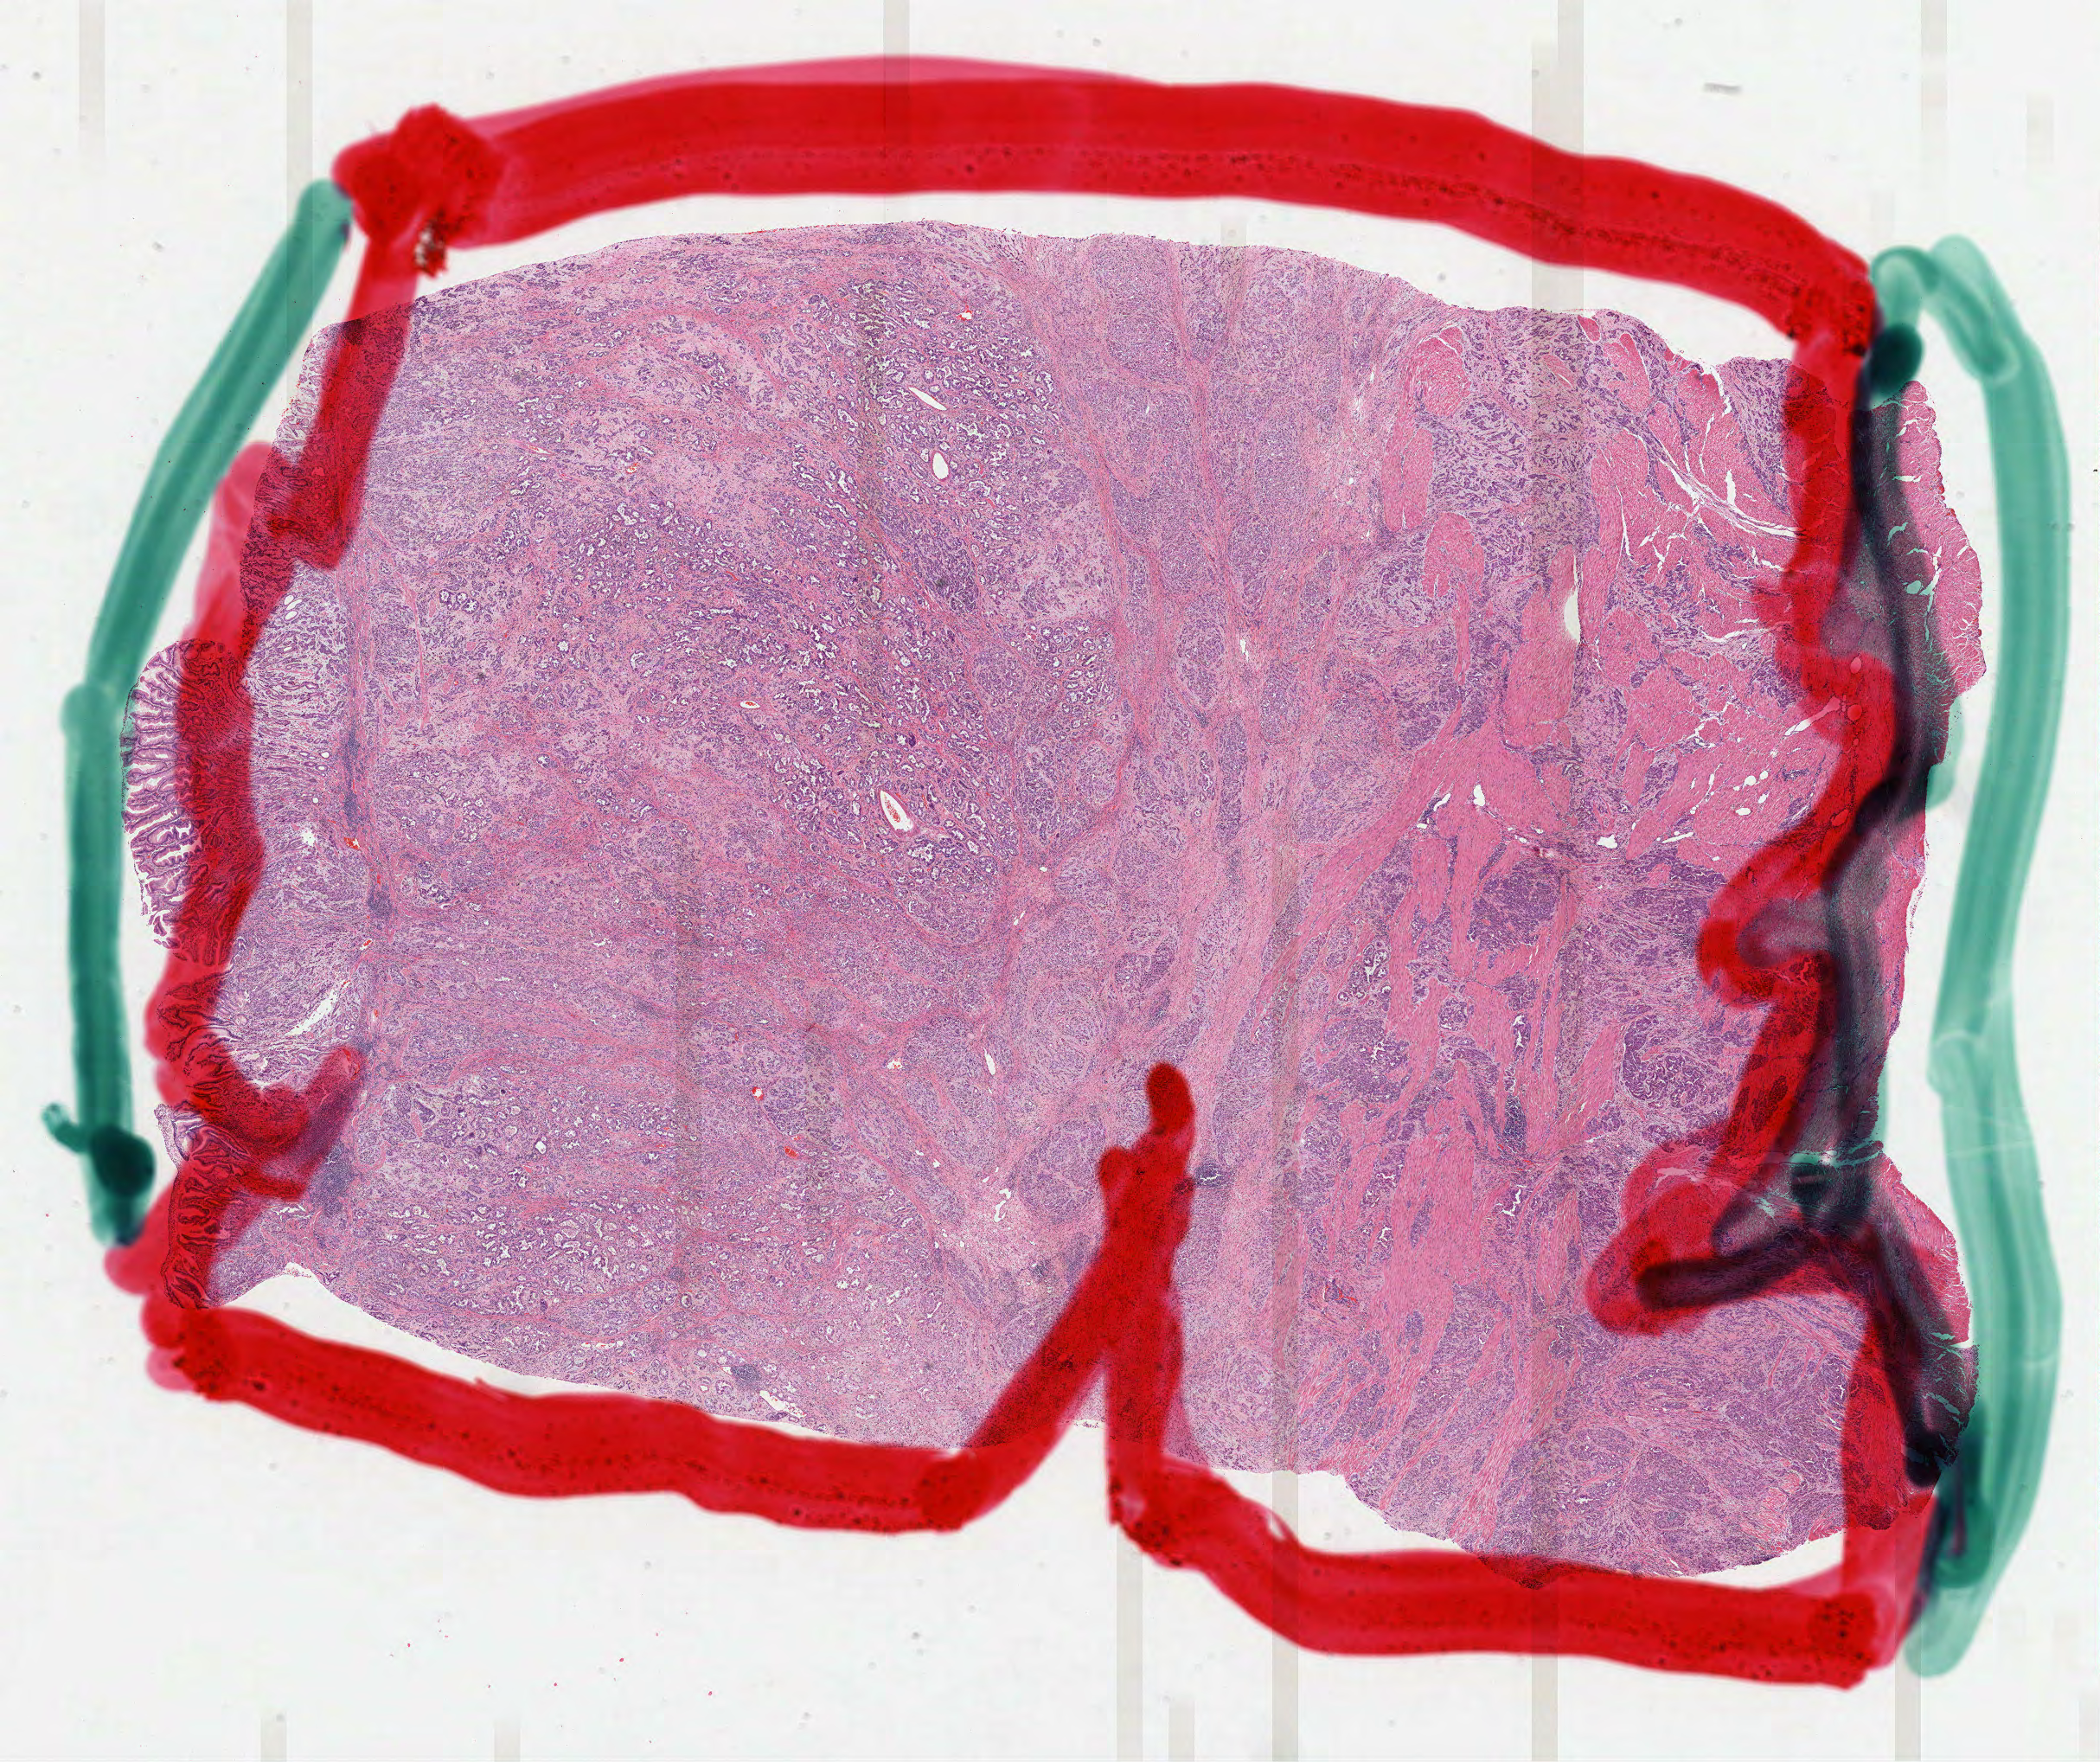
Digitized Hematoxylin and eosin (H&E) stained tissue section (whole slide), a low-resolution overview of the entire scanned area, about 19.6 x 16.4 mm; FFPE section; sample: primary tumour, stomach. Male patient; age at initial diagnosis 57 years. Histologic grade: G3 (poorly differentiated).
• lymph nodes positive (case pathology): 11 of 11 examined
• pathologic diagnosis: Adenocarcinoma, intestinal type
• AJCC pathologic stage: IV